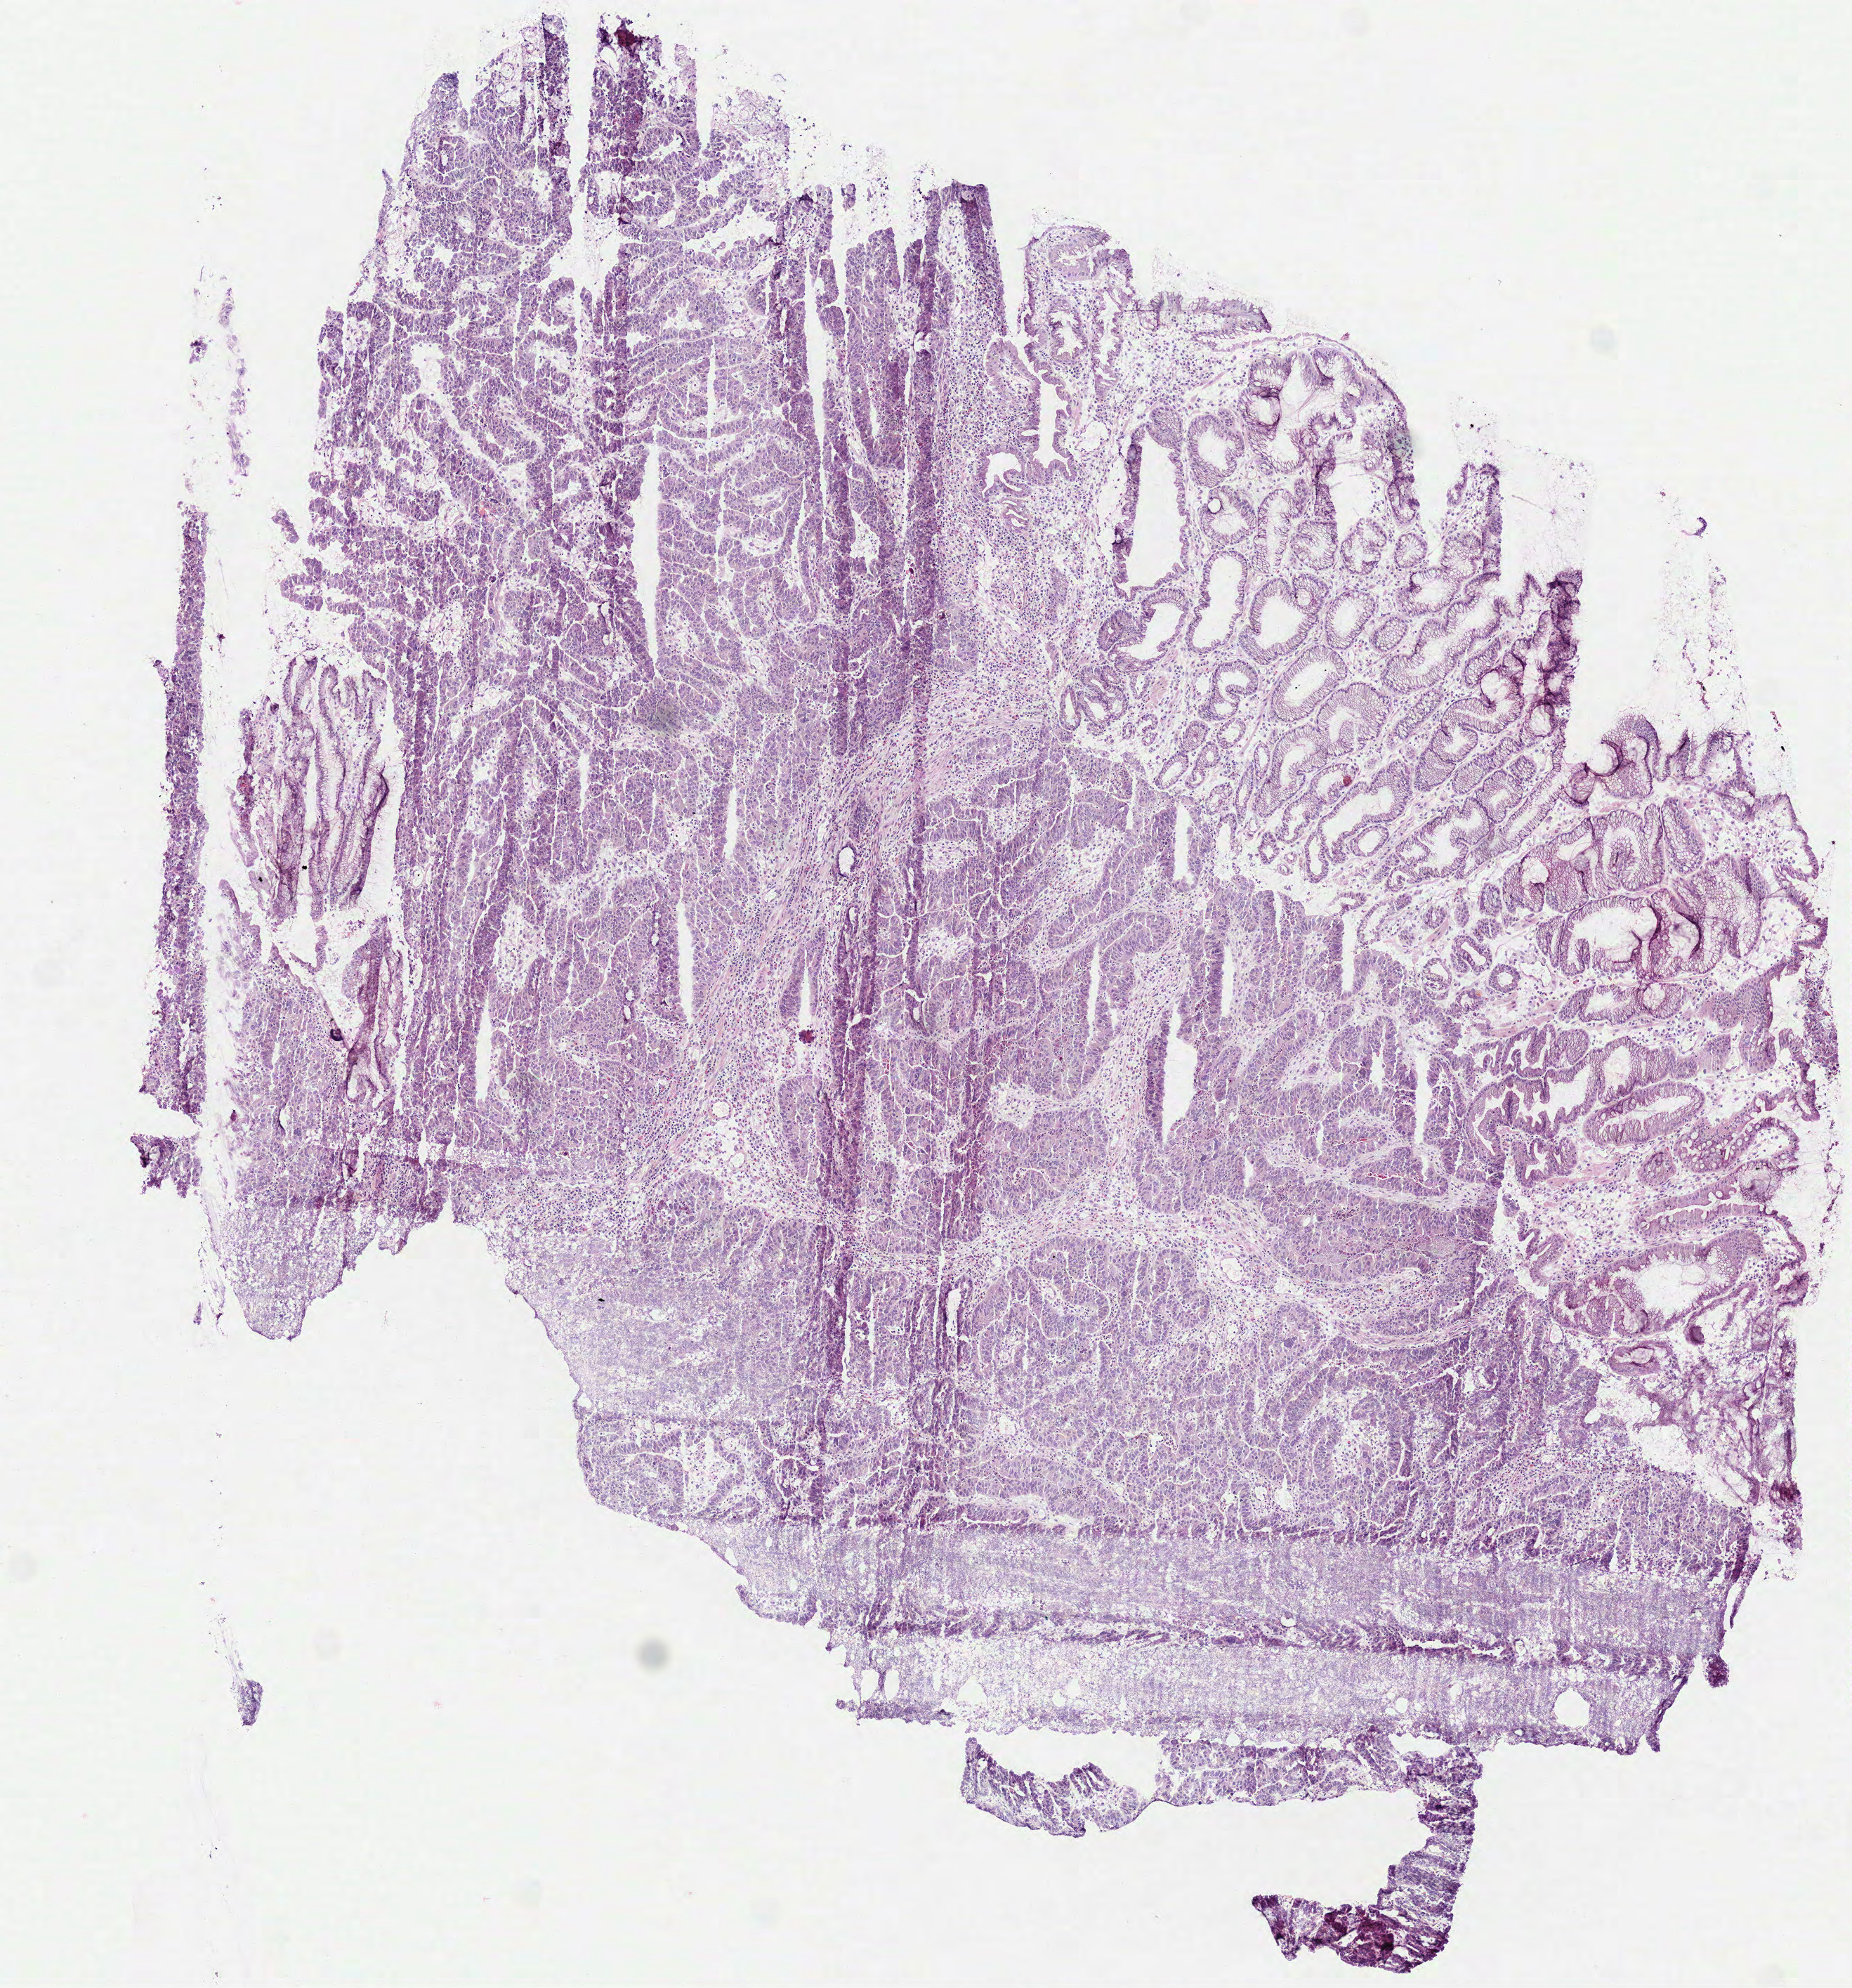
Hematoxylin and eosin (H&E) stained whole-slide image, a low-resolution overview of the entire scanned area, about 5.3 x 5.7 mm; frozen section; stomach, primary tumour sample. Male, age 77 years at initial diagnosis. Histologic grade: G2 (moderately differentiated). Composition of this section per pathologist review: tumour cells 63%, tumour nuclei 60%, normal cells 22%, stromal cells 15%, necrosis 0%.
- TNM: T2 N0 M0
- pathologic diagnosis: Tubular adenocarcinoma (body of stomach)
- lymph nodes positive (case pathology): 0 of 7 examined
- AJCC pathologic stage: IB (7th edition)